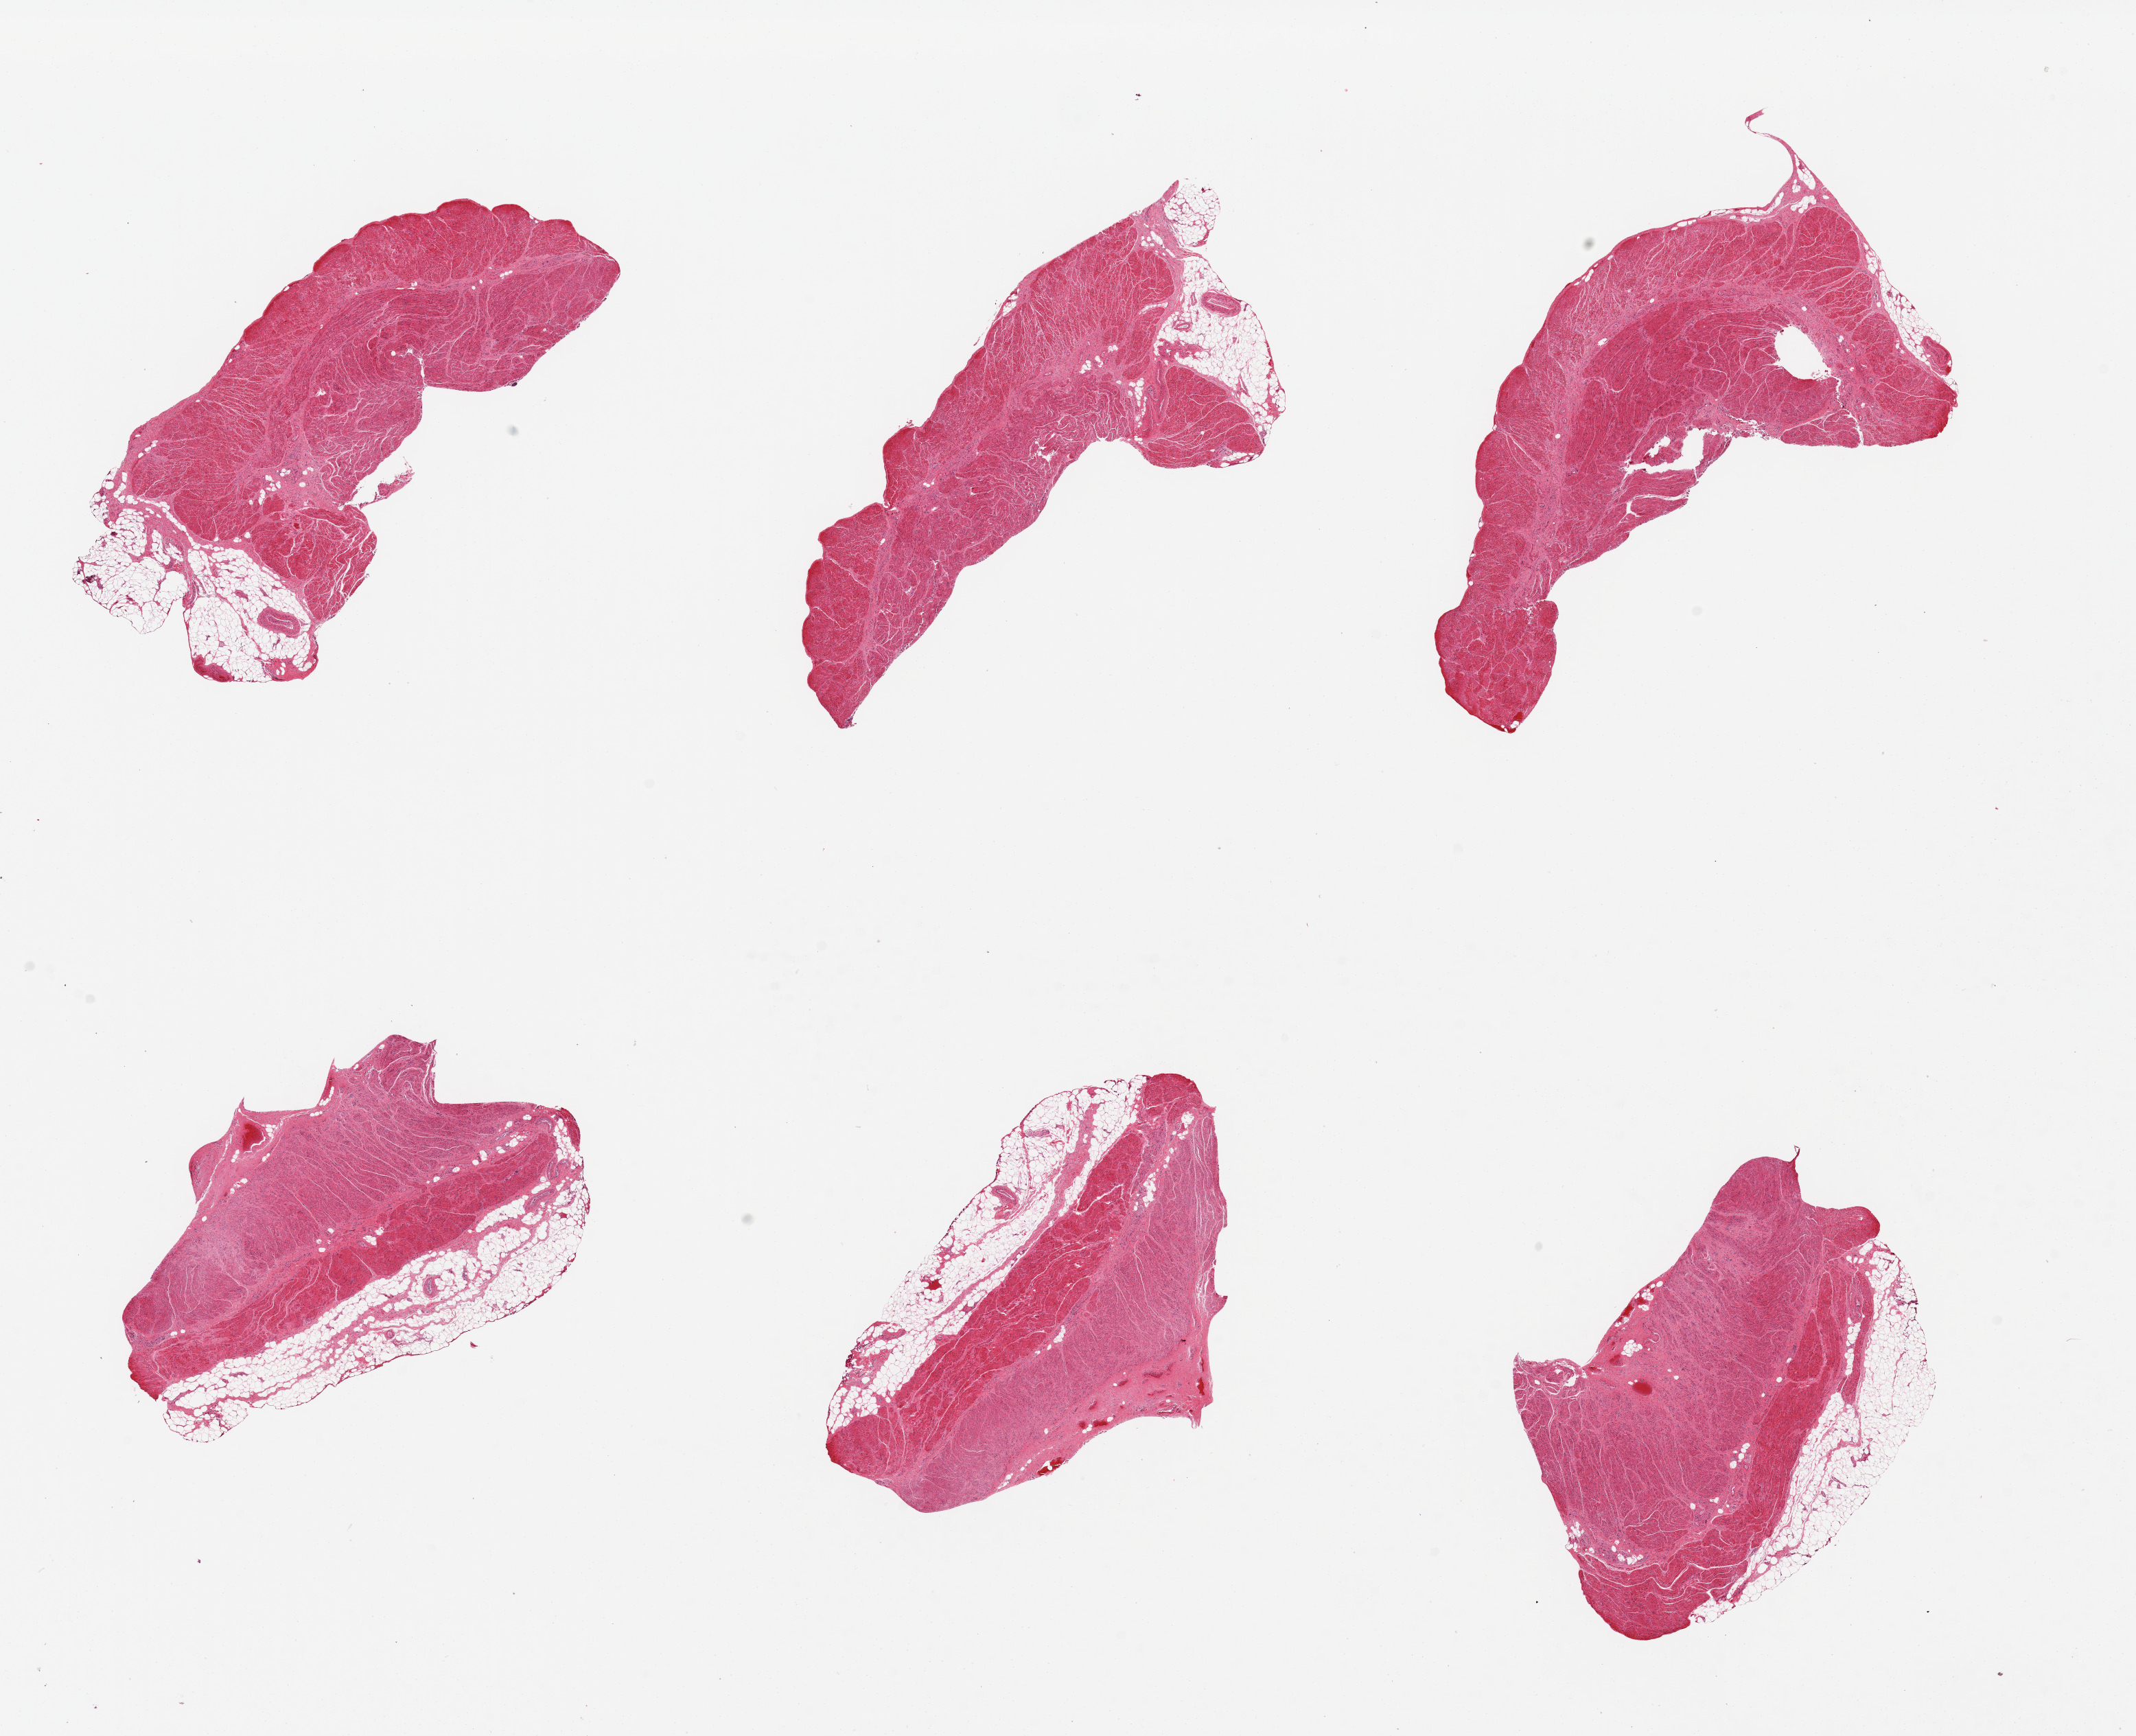
Whole-slide image, hematoxylin and eosin (H&E) stain — a low-resolution overview of the entire scanned area, about 24.6 x 20.0 mm; PAXgene-fixed paraffin-embedded (PFPE) section; target tissue: gastroesophageal junction; tissue donor sample.
- reviewer comment on this tissue sample: 6 pieces, all muscularus; adherent serosal fat up to ~1mm present on 4/6